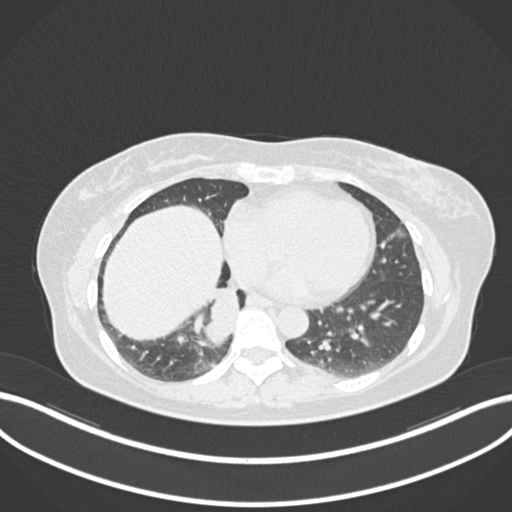
Chest CT, one axial slice. Lung window (W 1500 / L -600 HU). 1 mm slice thickness. 512 × 512 image matrix. Female patient, age 54 years. From the clinical record (not read from this slice): clinical TNM (as recorded): T4 N0 M0.
Structures marked on this image (rectangle marked by the reading radiologist):
- lung tumour (recorded histology: adenocarcinoma): box from (x=202, y=277) to (x=251, y=353) px